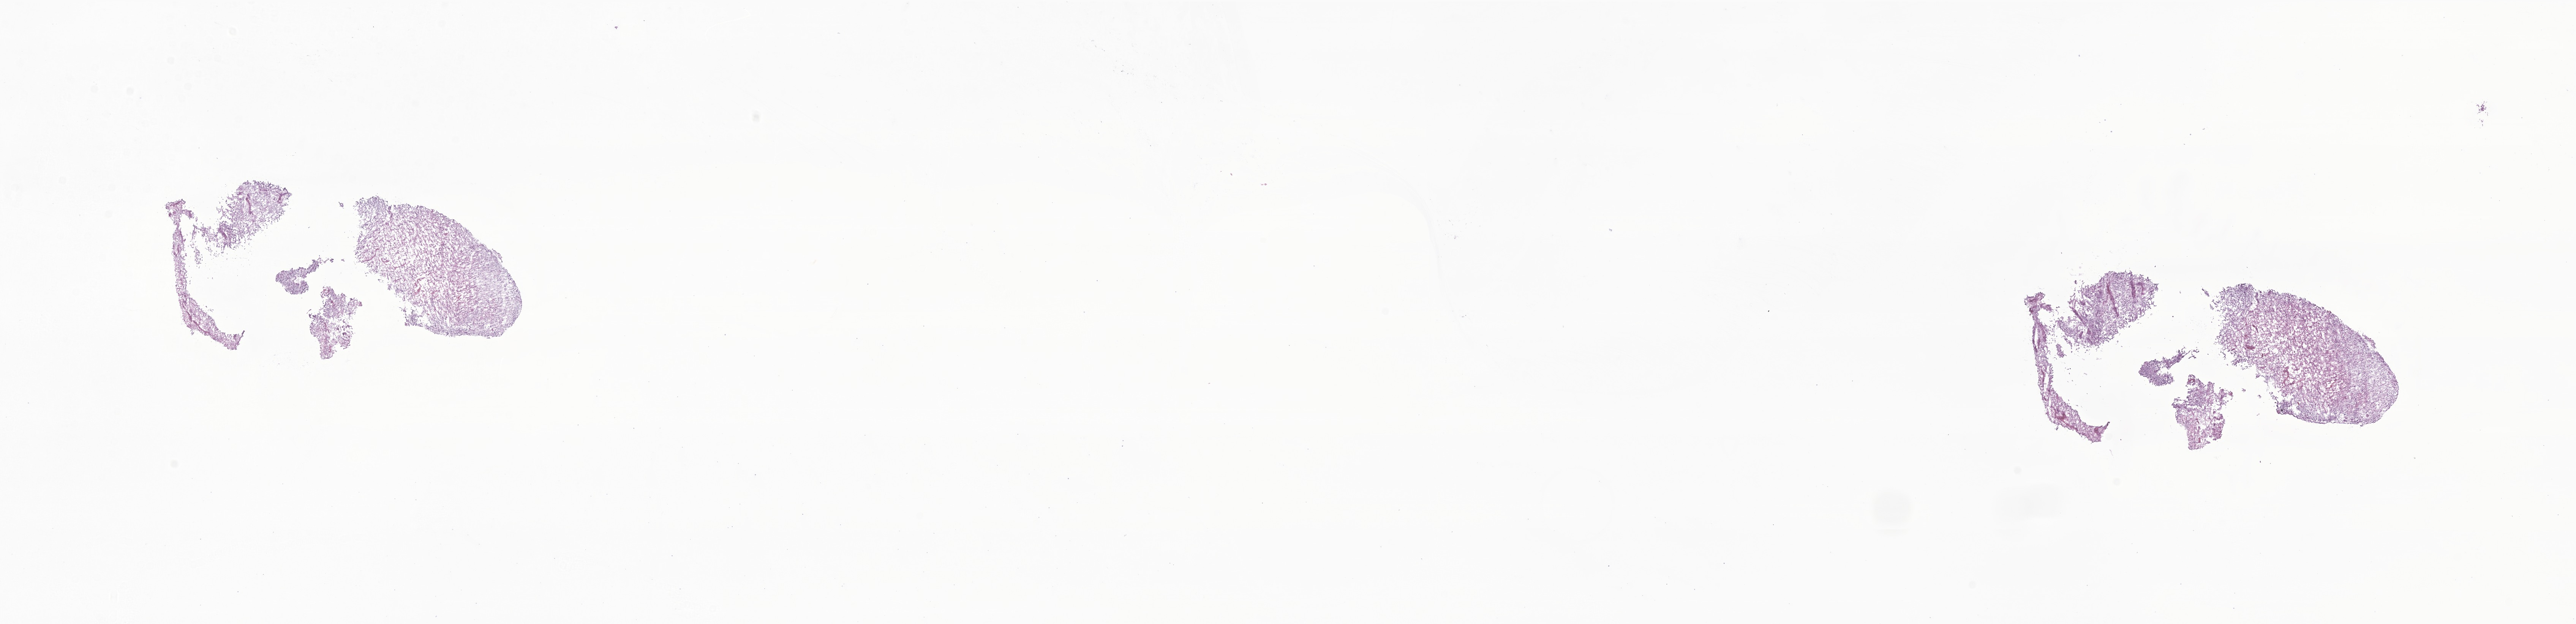
Digitized haematoxylin and eosin-stained section of tumor tissue from the central nervous system, whole scanned area (about 28.6 x 6.9 mm) shown as a low-resolution overview, frozen section (OCT-embedded). Patient: female, age 88 months (7 years 4 months).
Diagnosis (ICD-O-3 morphology term): Glioma, malignant.